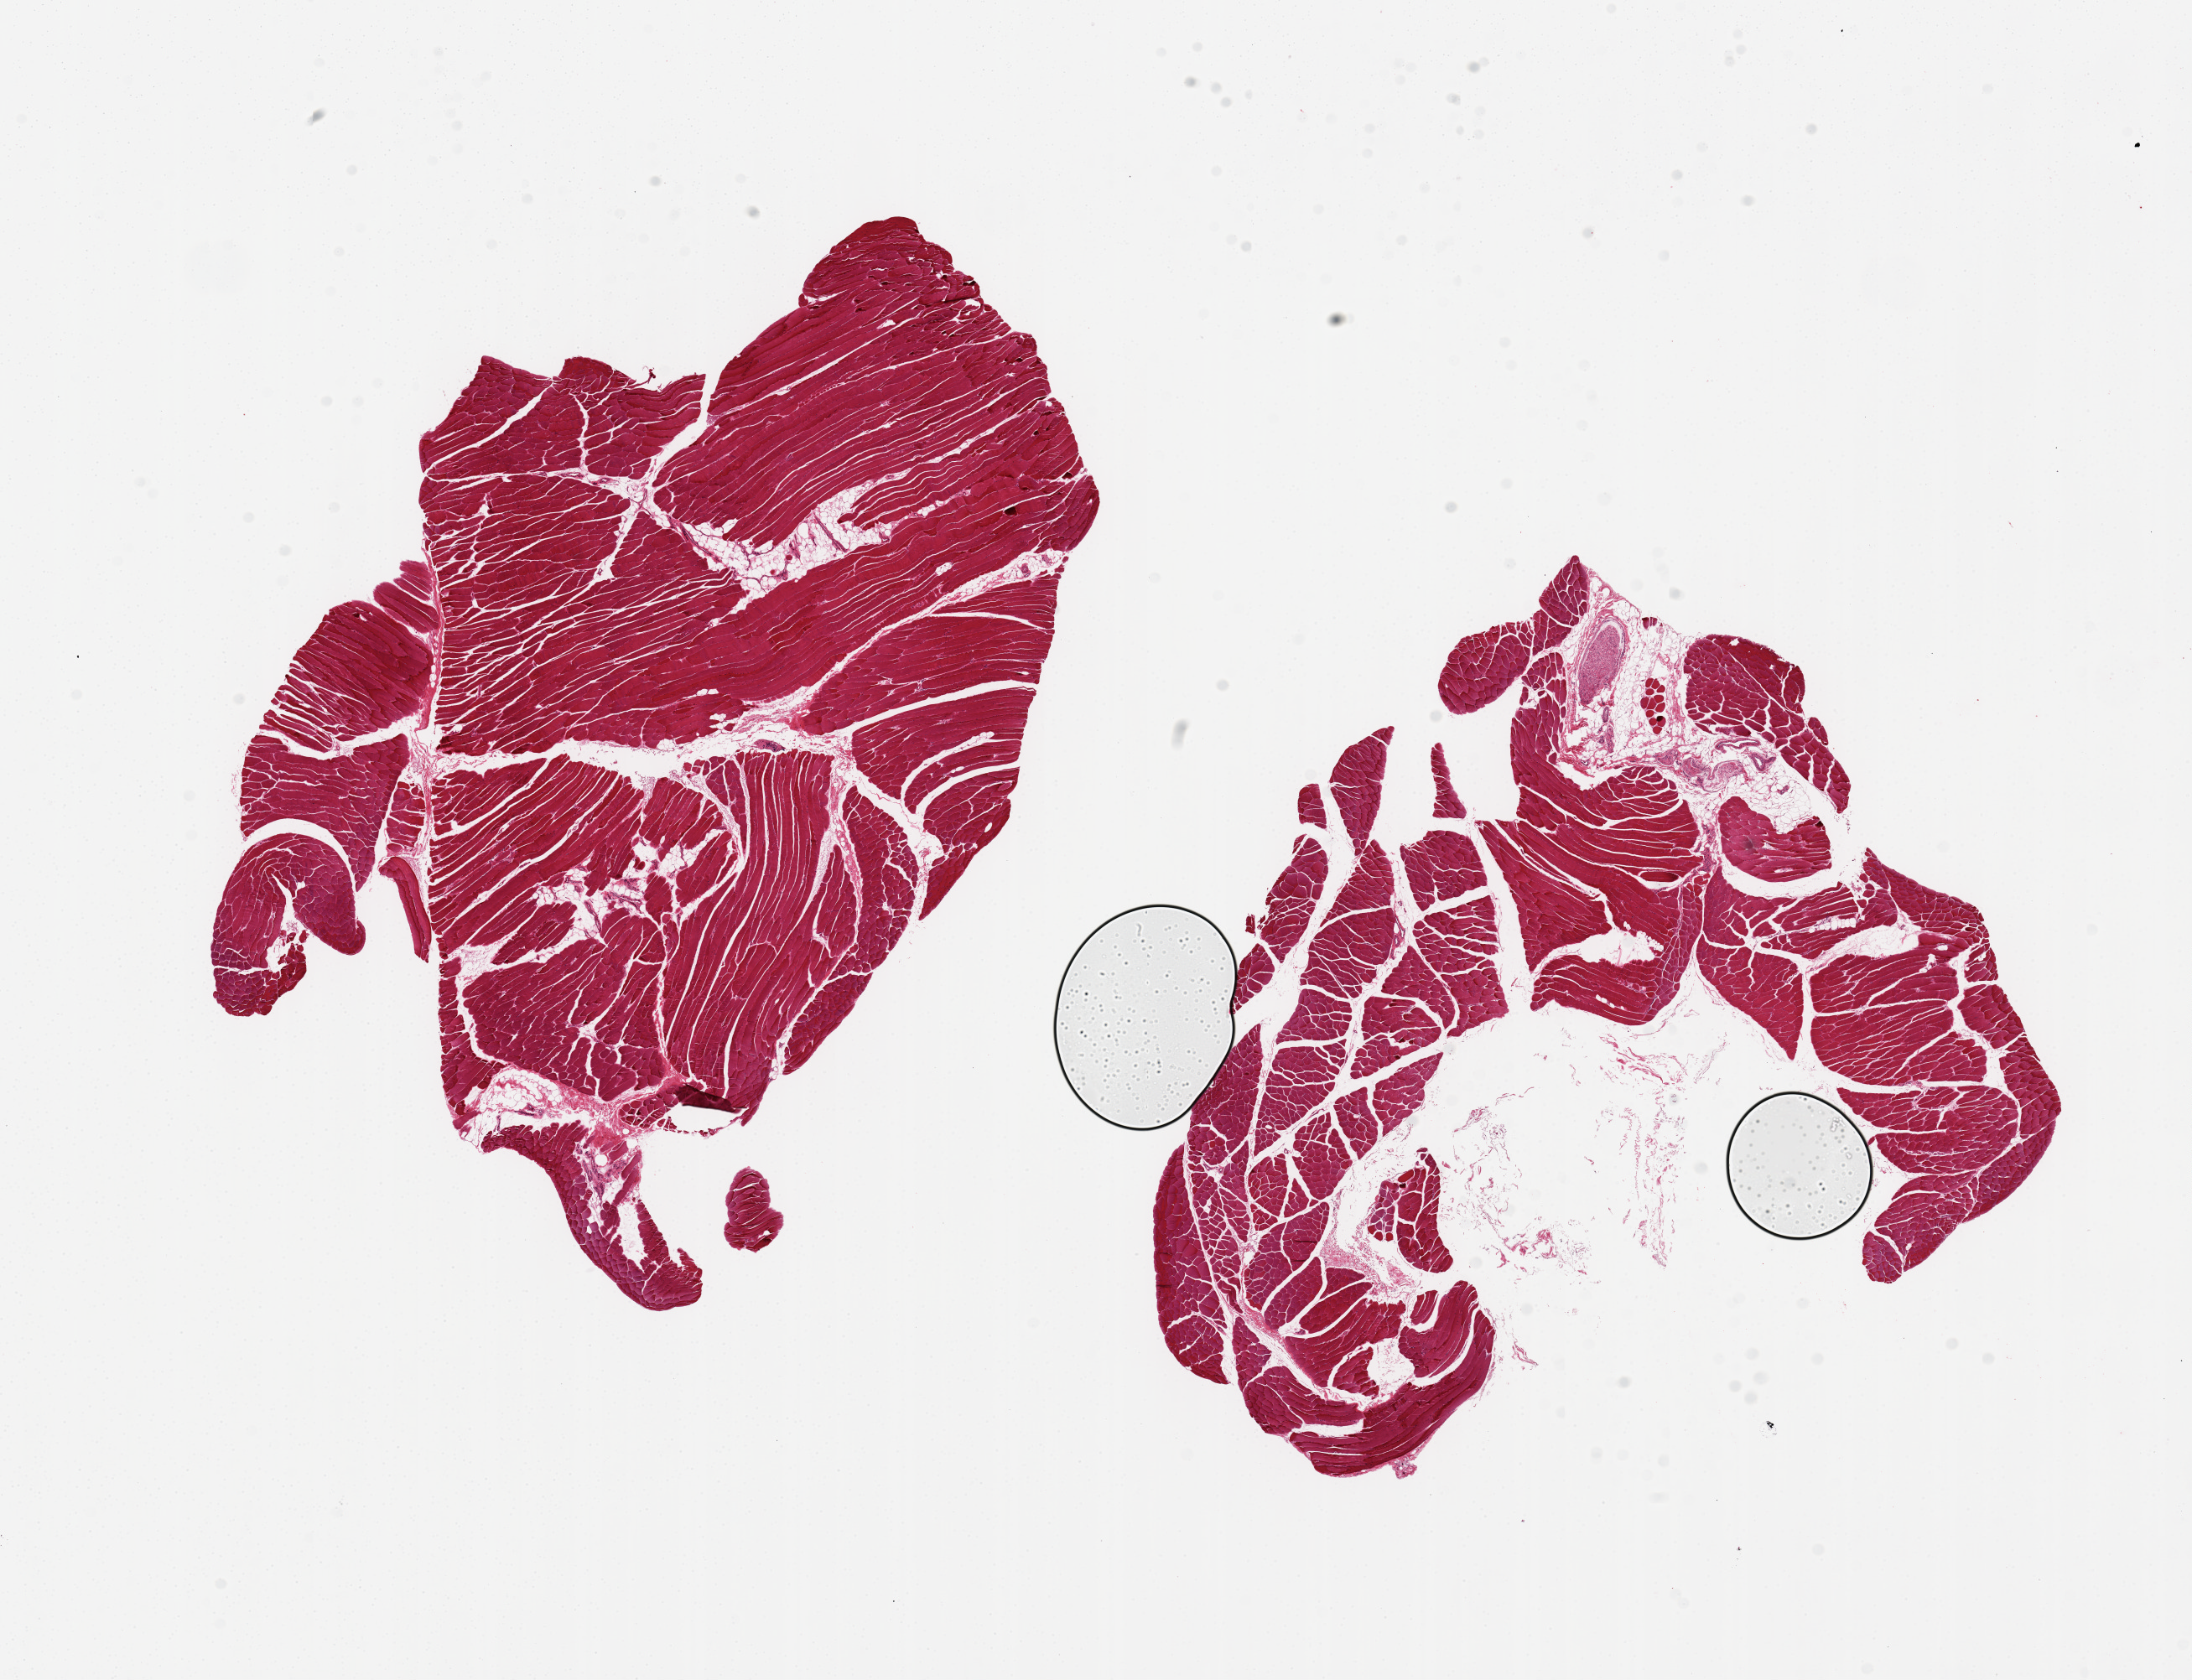
Digitized hematoxylin and eosin (H&E)-stained section, whole scanned area (about 20.7 x 15.8 mm) shown as a low-resolution overview; PAXgene-fixed paraffin-embedded (PFPE) section; section of skeletal muscle (target tissue); tissue donor sample. Donor: male.
Review note (as recorded): 2 pieces, 9x6.5 and 8.5x7mm; <5% interstitial fat.